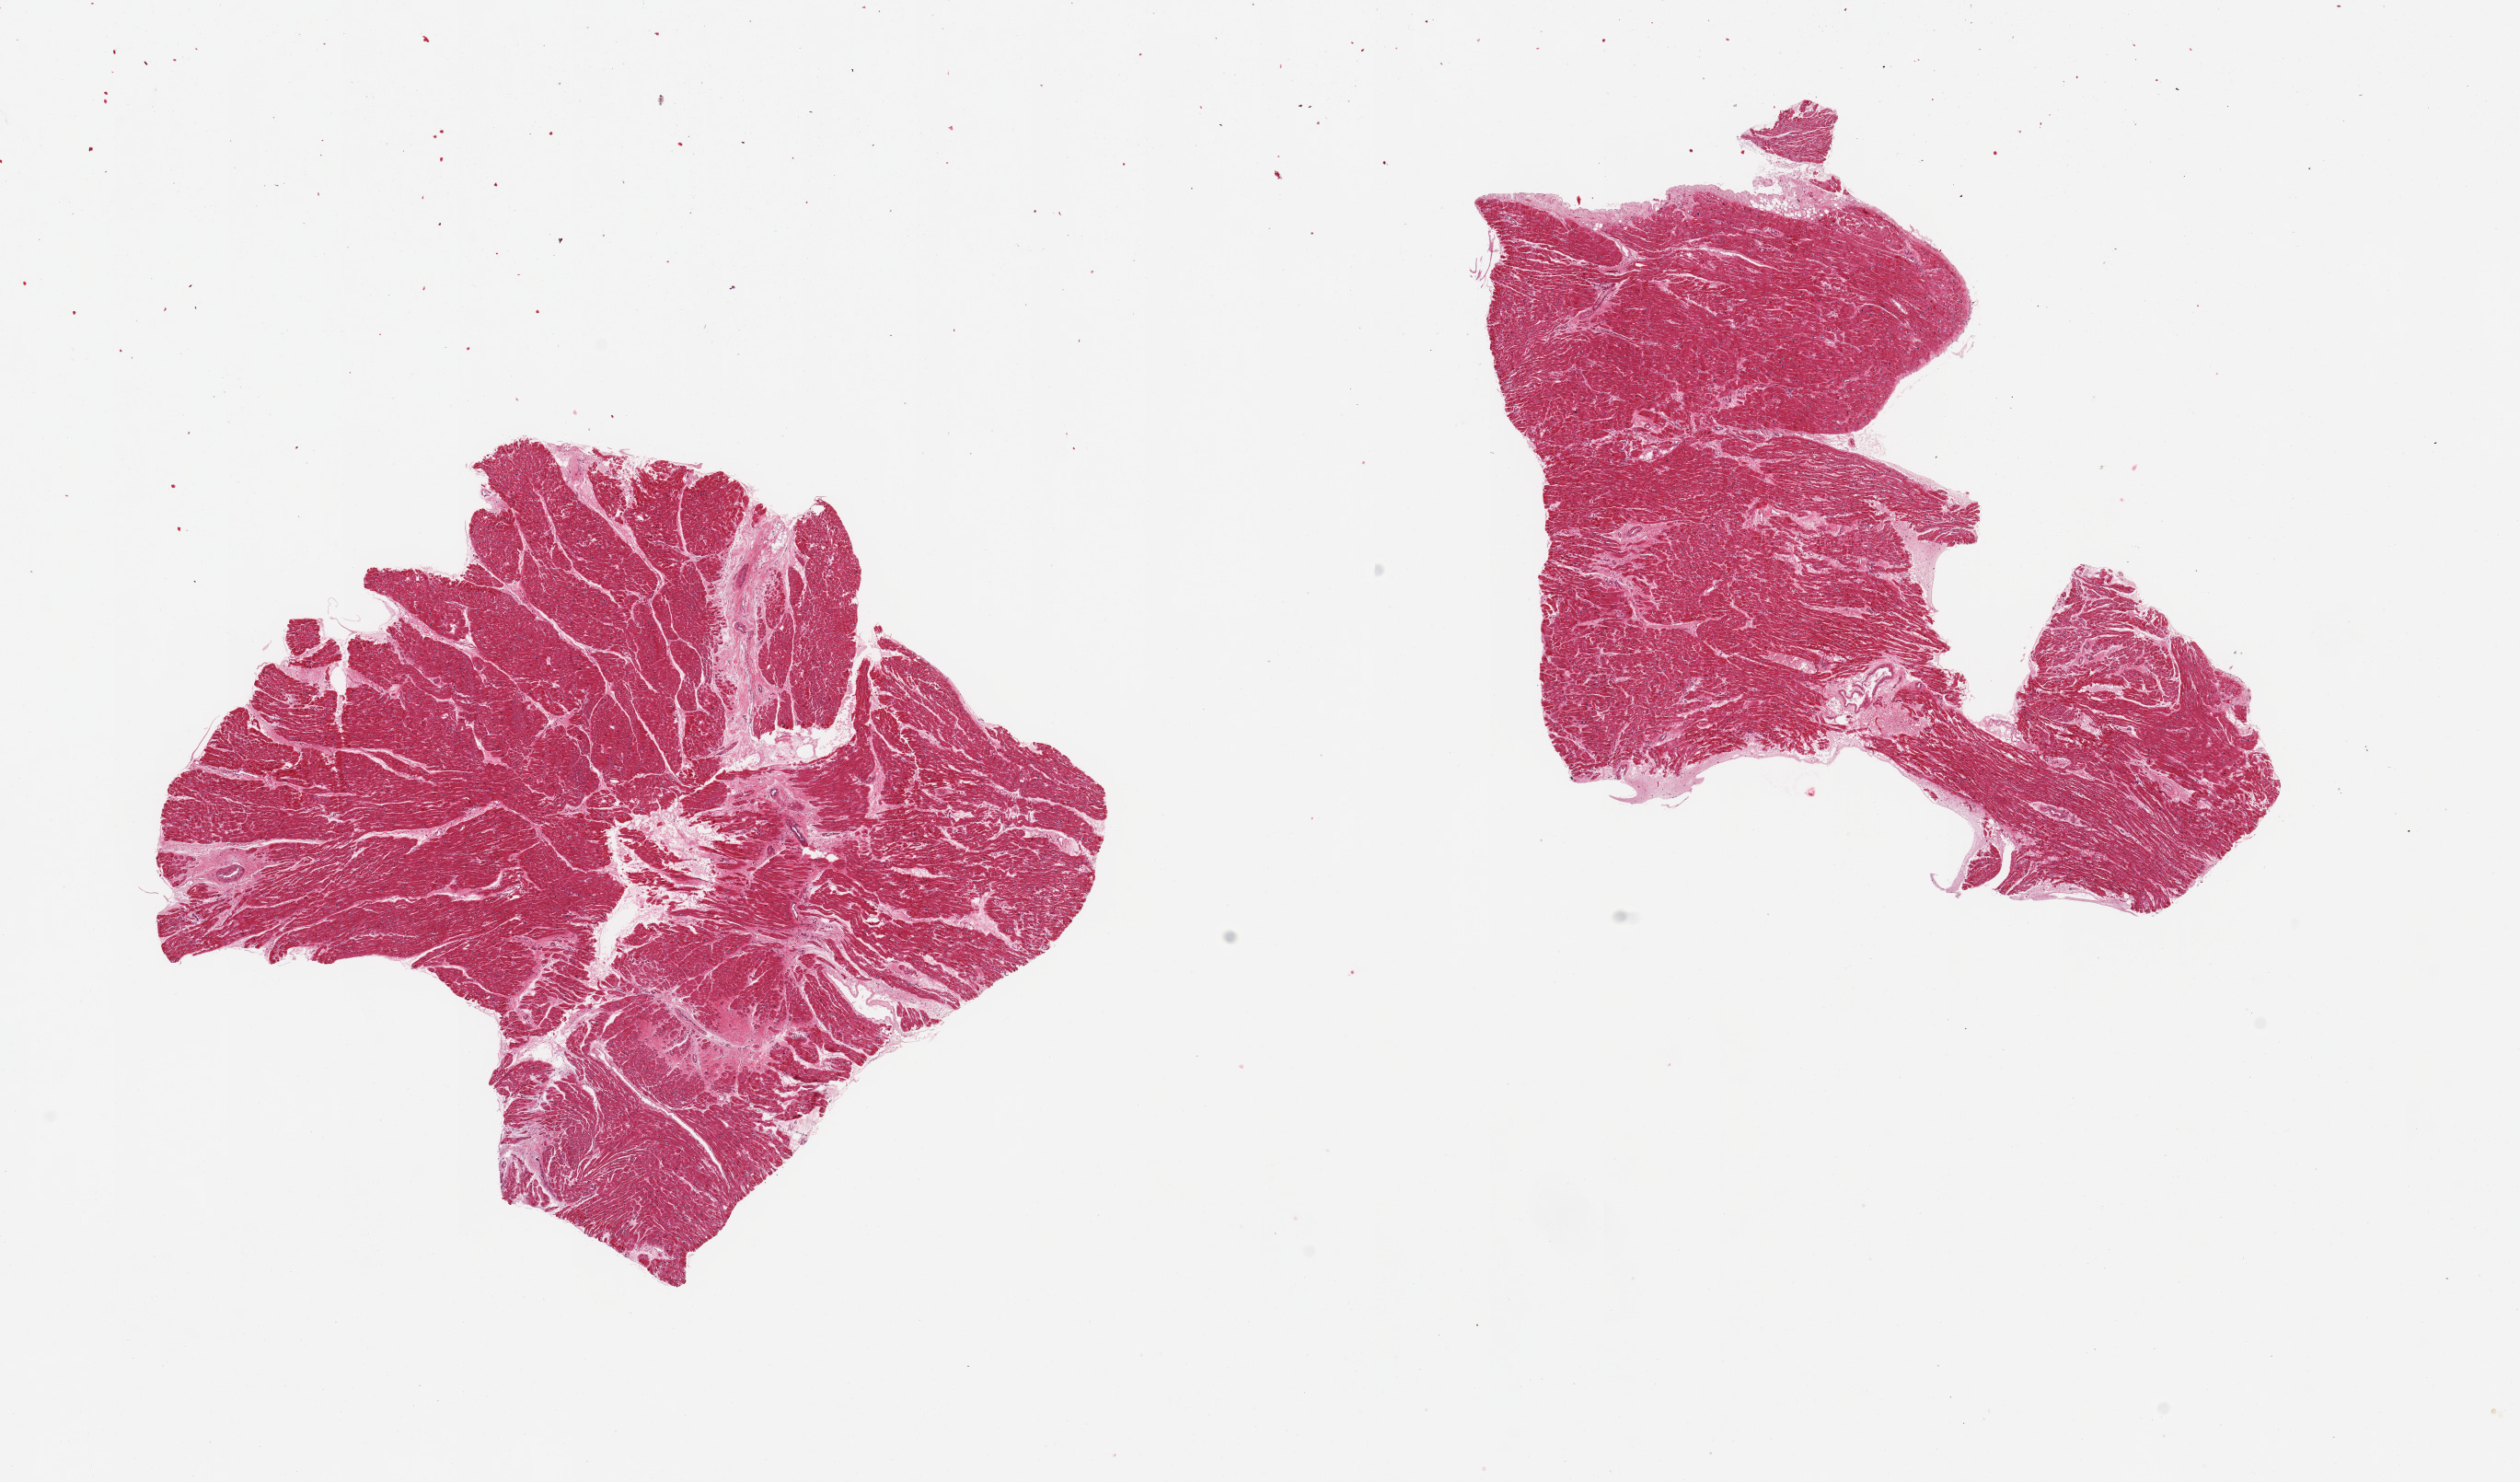
Digitized hematoxylin and eosin (H&E)-stained section — low-resolution overview of the scanned area, about 21.7 x 12.7 mm, PAXgene-fixed, paraffin-embedded tissue, sampled site (target tissue): heart, tissue donor sample. Donor sex: female.
* reviewer comment on this tissue sample: 2 pieces, myocardium with interstitial fibrosis and remote microinfacts